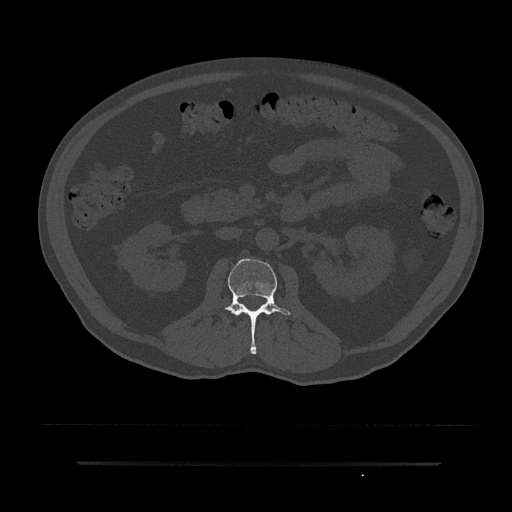
CT including the spine, one axial slice; slice 75 of 797 in the series (ordered by position); reconstruction kernel Br40s/3; 120 kVp; bone window (W 1800 / L 400 HU); 0.5 mm slice thickness; 512 × 512 image matrix, field of view 464 × 464 mm. Patient: male, 59 years. From the clinical record (not read from this slice): primary cancer: bile ducts.
Structures marked on this image (semi-automatically segmented with operator editing):
- L2 vertebra: bounding box (x1, y1, x2, y2) in pixels: (223, 258, 301, 354)